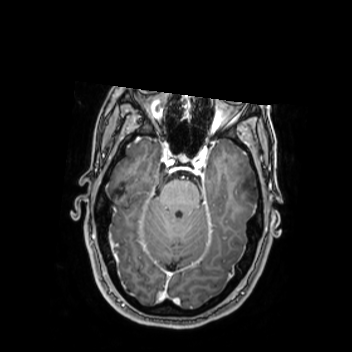
Brain MRI from a brain-tumour surgery series, one axial slice. Slice 172 of 350 in the series (ordered by position). T1-weighted post-contrast. 0.9 mm slice thickness. 352 × 352 image matrix, field of view 280 × 280 mm. From the clinical record (not read from this slice): histopathology: Oligodendroglioma; WHO grade: 2; IDH mutation: yes.
Outlined on this slice (outlined manually by an expert reader):
- tumour: bounding box [x1, y1, x2, y2] px = [228, 166, 256, 213]